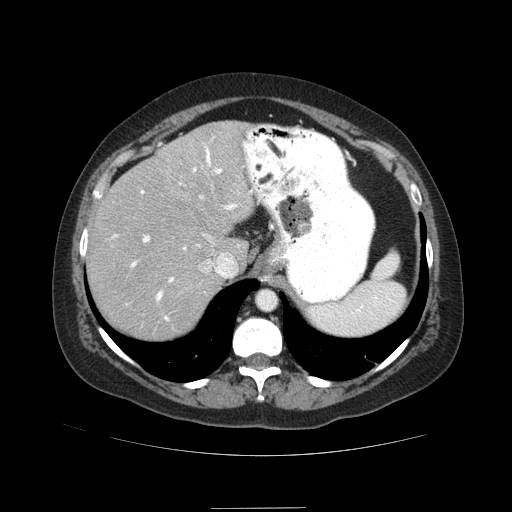
Contrast-enhanced abdominal CT (liver protocol), one axial slice; slice 66 of 89 in the series (ordered by position); soft-tissue window (W 400 / L 40 HU); 2.5 mm slice thickness; 512 × 512 image matrix, field of view 400 × 400 mm. Case-level facts recorded for this patient, not image findings: diagnosis: hepatocellular carcinoma (patient treated with transarterial chemoembolisation; whether this scan precedes or follows treatment is not stated here); TNM stage (as recorded): Stage-IIIB; Child-Pugh class: A; tumour nodularity: multinodular.
Outlined on this slice (semi-automatically segmented with operator editing):
- abdominal aorta: bounding box <258,291,276,309> (left, top, right, bottom; pixels)
- liver parenchyma outside the tumour (the mass and vessels are separate outlines, so this box may not span the whole liver): <86,120,254,338>
- liver vessels: <113,145,237,321>